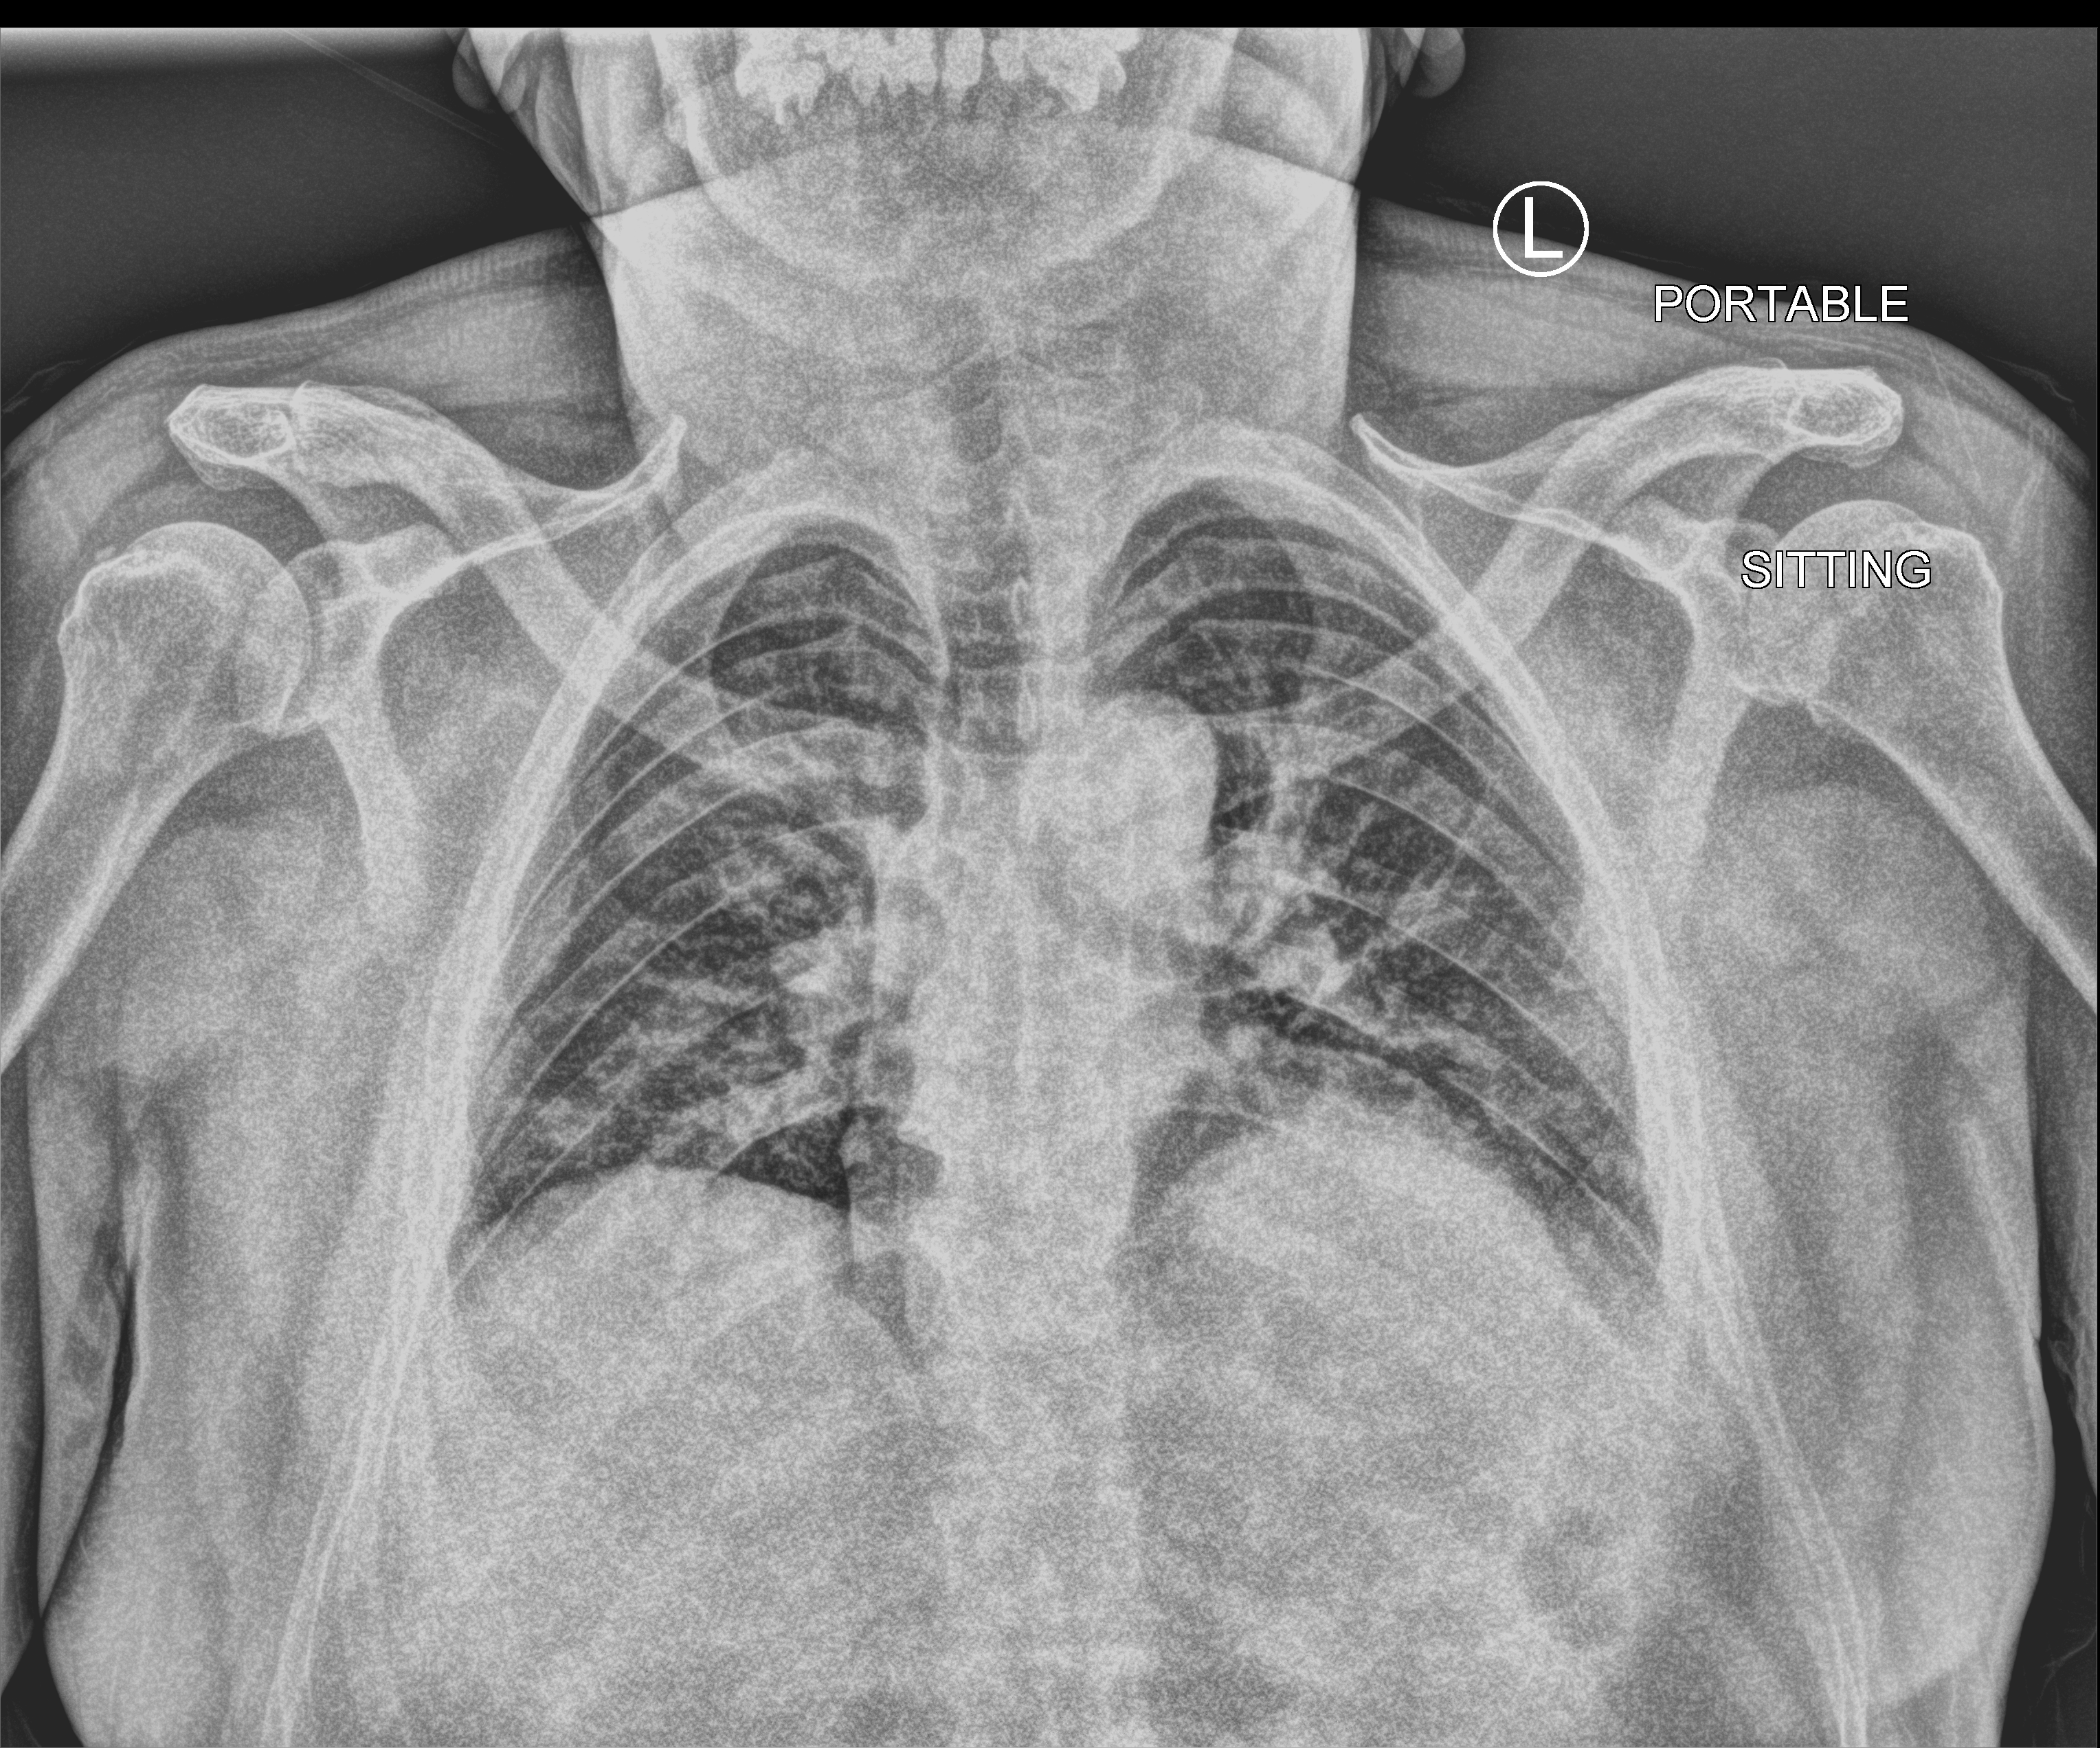
Portable chest radiograph, anteroposterior (AP) projection. Male patient hospitalised with COVID-19, age 60–74 years.
Admission-level facts for this patient (not findings on this image; timing relative to this image not recorded): length of hospital stay: 12 days; smoking status (admission record): never.